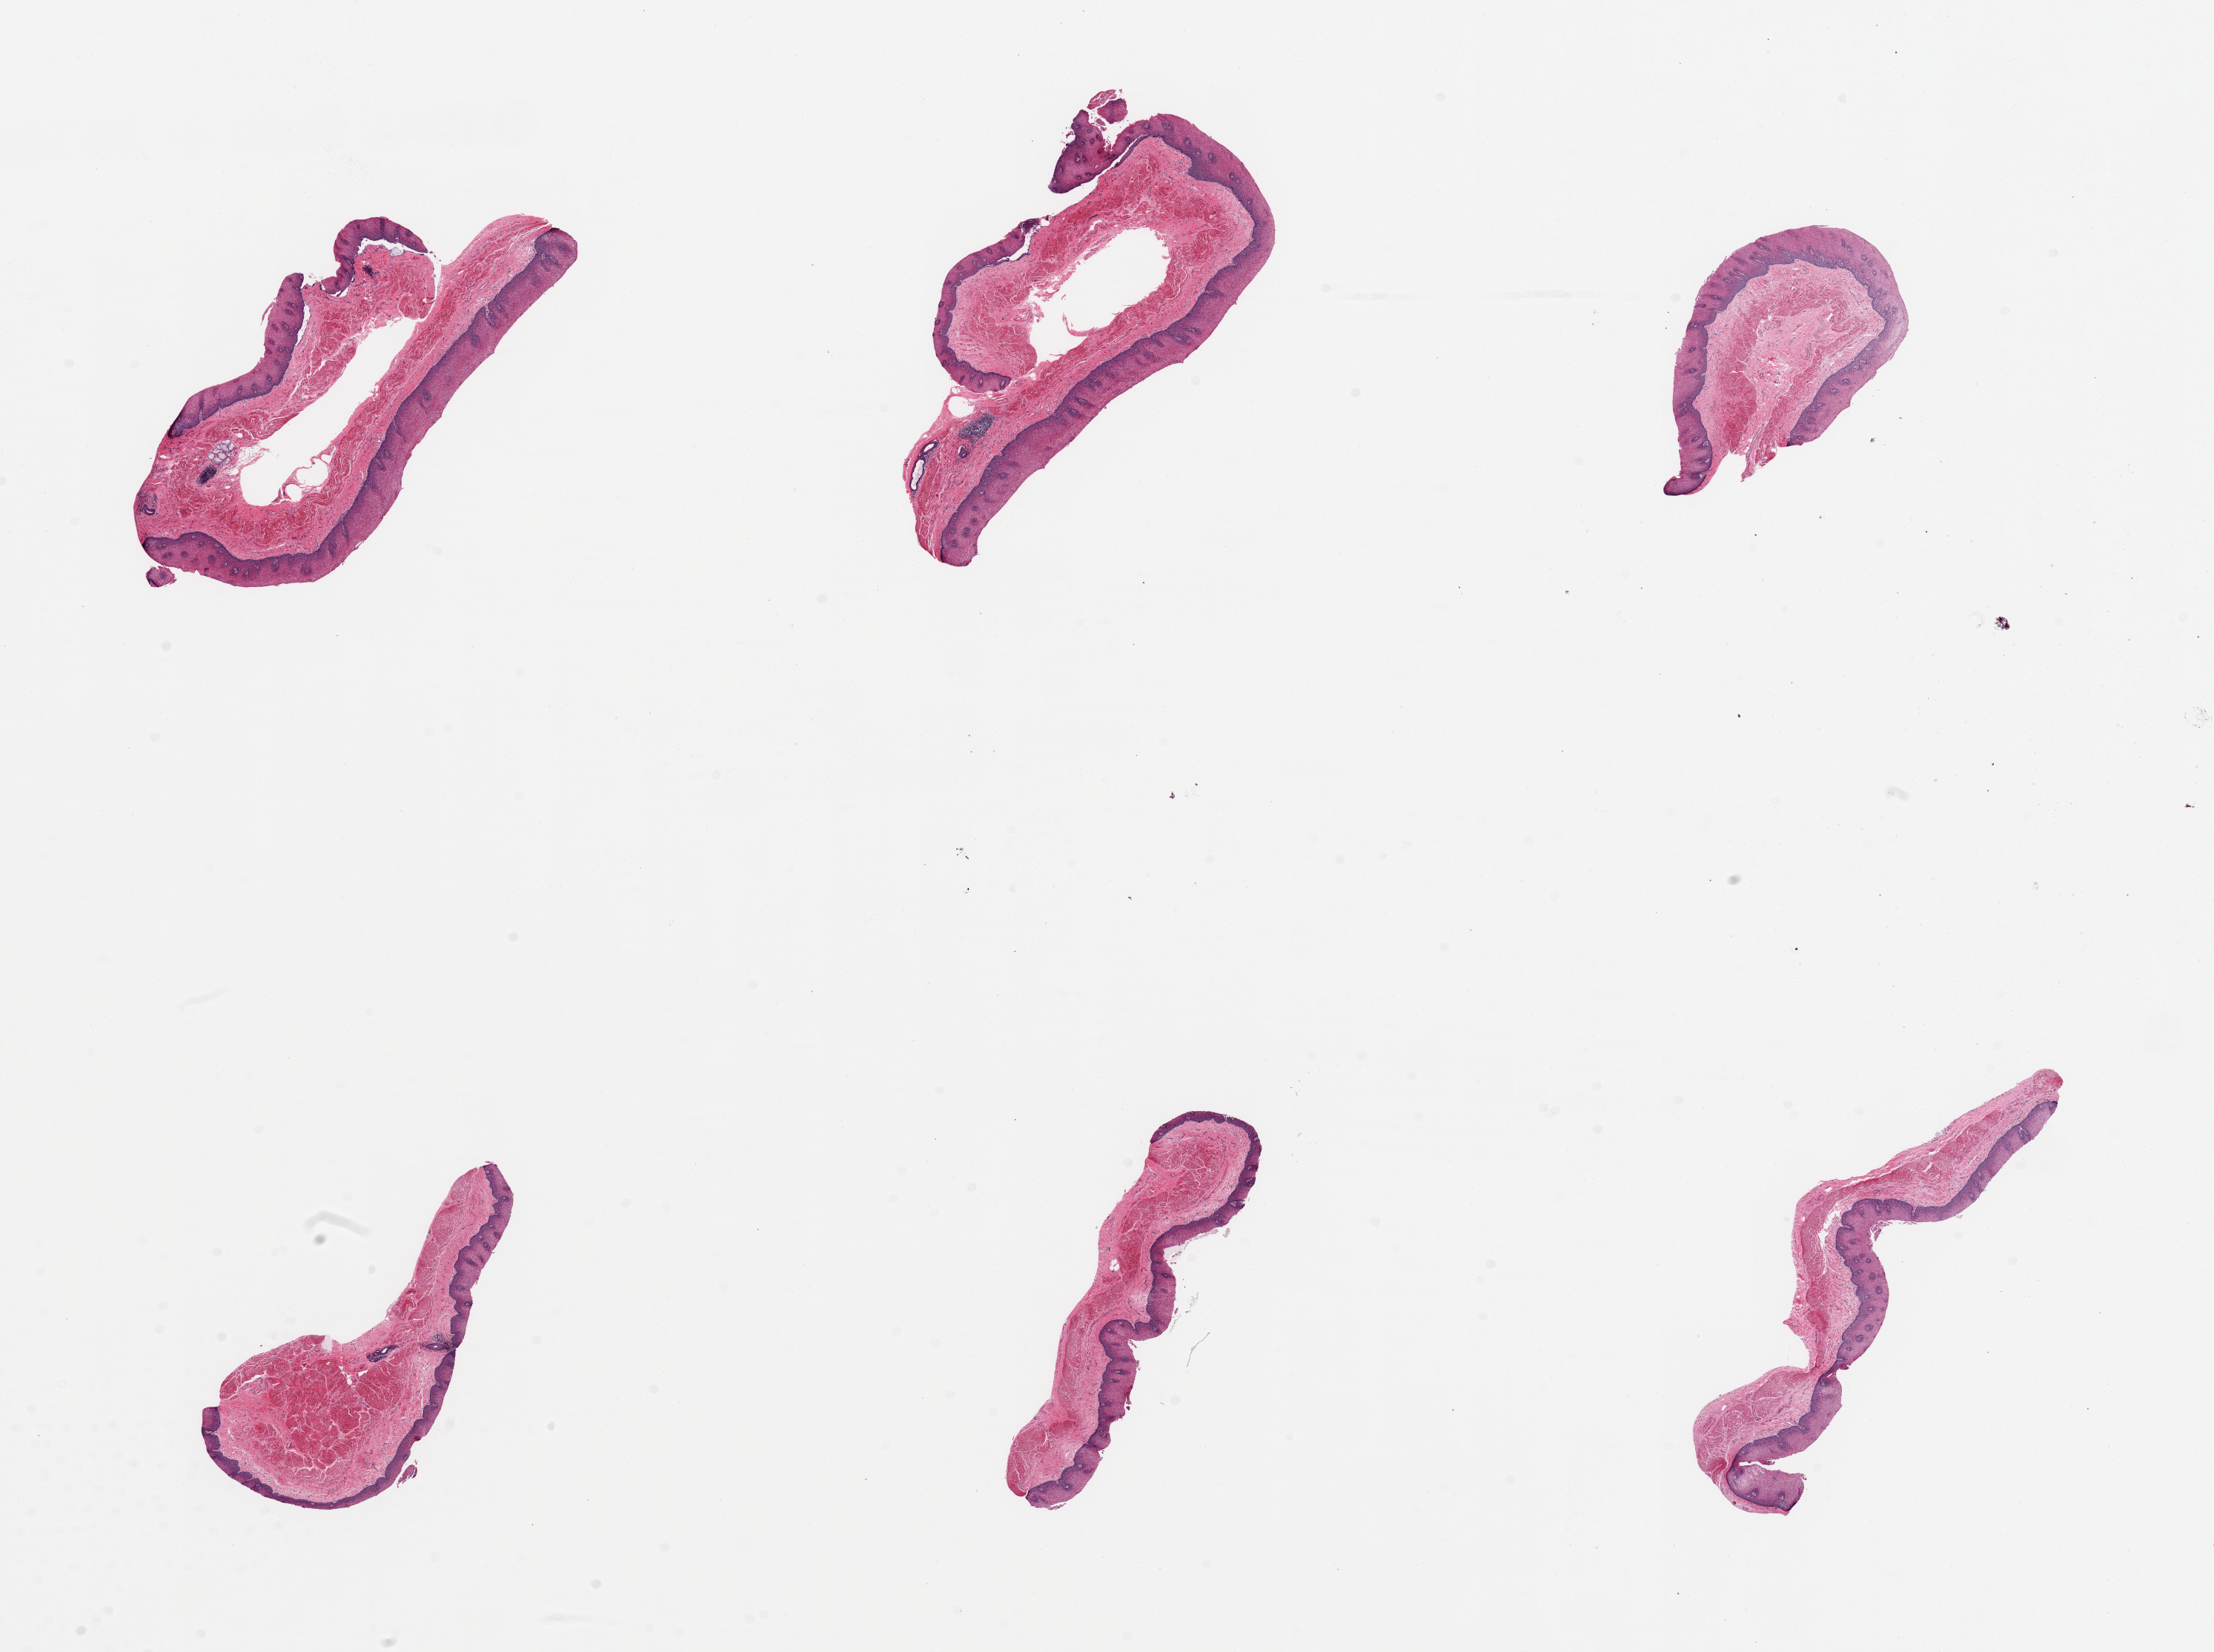
Haematoxylin and eosin whole-slide image, low-resolution overview of the scanned area, about 23.6 x 17.6 mm. PAXgene-fixed, paraffin-embedded tissue. Target tissue: esophageal mucous membrane. Donor tissue sample. Donor sex: female.
Reviewer comment on this tissue sample: 6 pieces.